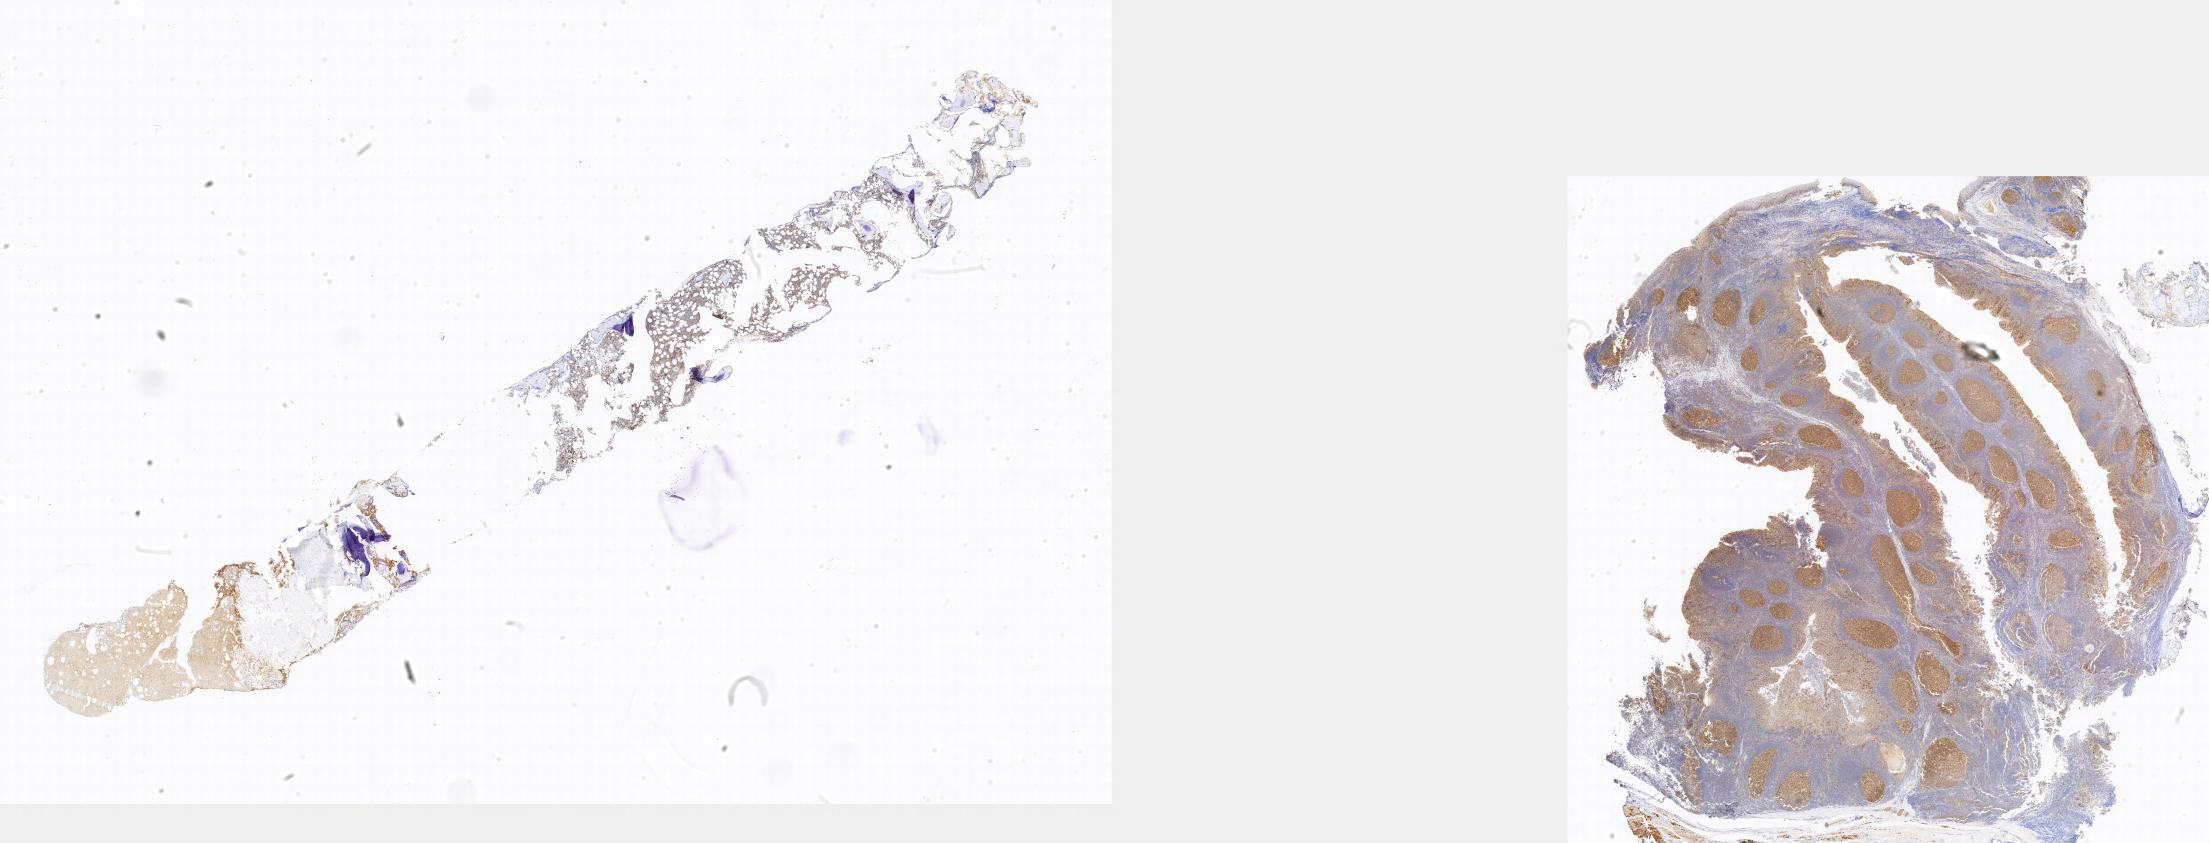
Whole-slide image, immunohistochemical stain for BCL6 — a low-resolution overview of the entire scanned area; specimen: tumor tissue; anatomic site: bone marrow. Patient male; age 15 years.
Histologic diagnosis: Burkitt lymphoma, NOS.